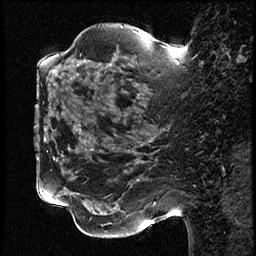
Breast MRI (dynamic contrast-enhanced), one sagittal slice. Slice 29 of 78 in the series (ordered by position). Dynamic contrast-enhanced study with each time point stored as its own series, time point 2 of 3 at this slice position (early post-contrast, ordered by acquisition time). 1.5 T. TE 4.2 ms, TR 17.6 ms. 256 × 256 image matrix, field of view 200 × 200 mm. Female patient, age 42 years. Case-level facts recorded for this patient, not image findings: setting: breast cancer imaged before/during neoadjuvant chemotherapy; receptor status: HER2-positive.
Outlined on this slice (semi-automatic segmentation, software-assisted and operator-edited):
- analysis volume of interest (the breast-tissue region the enhancement analysis was run in; not a lesion): box from (x=50, y=48) to (x=131, y=129) px
- tumour enhancement mask (voxels above the 100 % enhancement threshold inside the analysis volume of interest): (x=52, y=70)–(x=55, y=72)